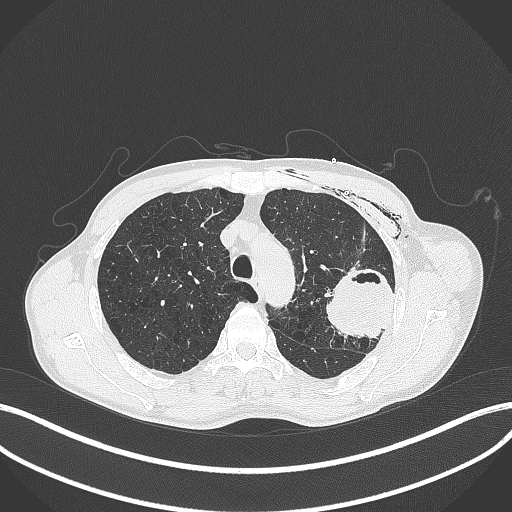
Chest CT, one axial slice; slice 306 of 457 in the series (ordered by position); 120 kVp; lung window (W 1500 / L -600 HU); 1 mm slice thickness; 512 × 512 image matrix, field of view 400 × 400 mm. Patient: male, 58 years. Case-level facts recorded for this patient, not image findings: clinical TNM (as recorded): T3 N0 M0.
Outlined on this slice (rectangle marked by the reading radiologist):
- lung tumour (recorded histology: adenocarcinoma): box from (x=323, y=265) to (x=396, y=347) px